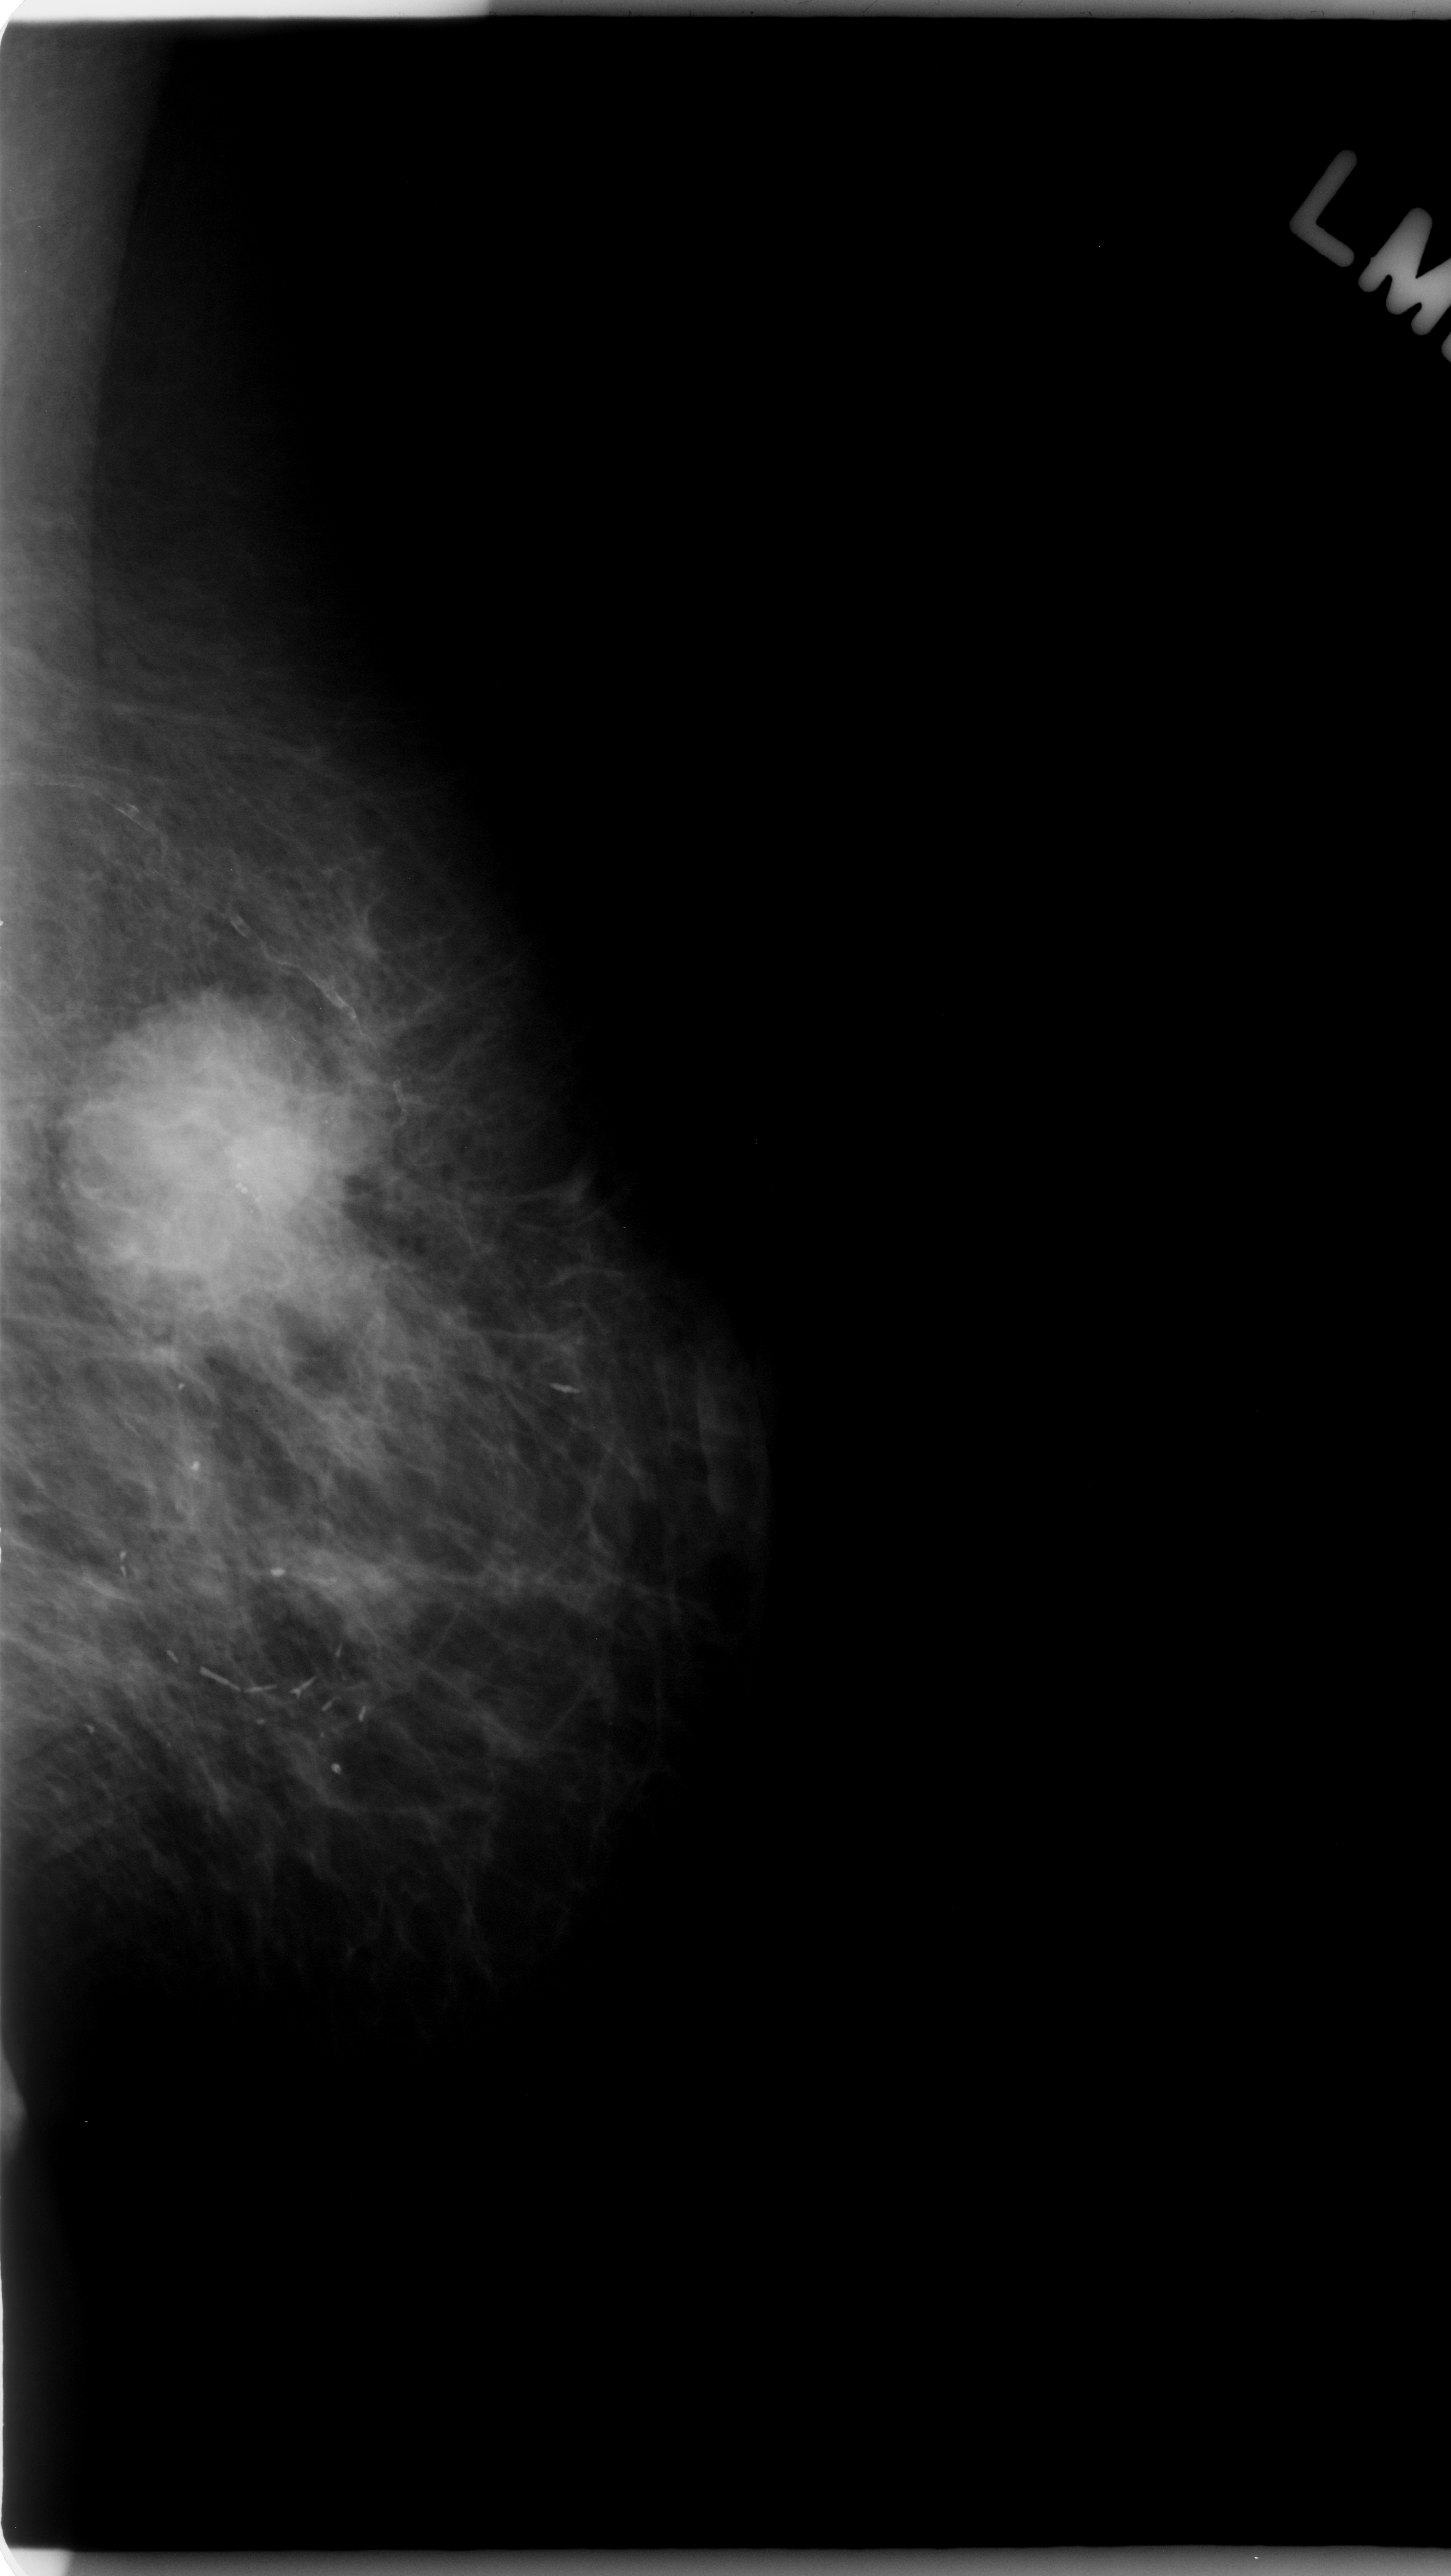
Mammogram (digitized film); left breast; MLO view; breast composition: almost entirely fatty (BI-RADS density category 1 of 4).
Radiologist-marked abnormalities on this image: mass, shape lobulated, margins microlobulated; BI-RADS assessment category 5; subtlety rating 5 on a 1 (subtle) to 5 (obvious) scale; pathology result (as recorded, not read from the image): malignant.